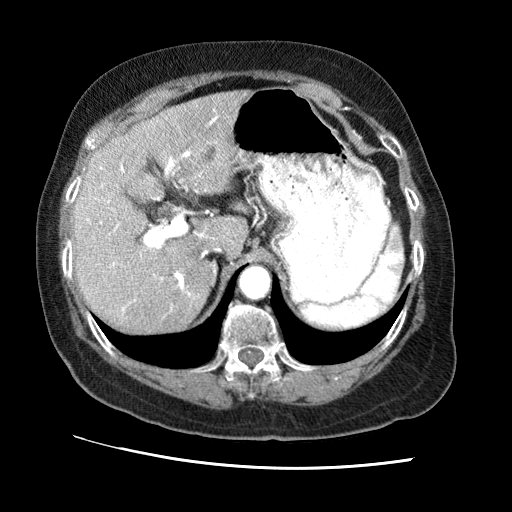
Contrast-enhanced abdominal CT (liver protocol), one axial slice; slice 44 of 65 in the series (ordered by position); reconstruction kernel STANDARD; 120 kVp; soft-tissue window (W 400 / L 40 HU); 2.5 mm slice thickness; 512 × 512 image matrix, field of view 340 × 340 mm. Case-level facts recorded for this patient, not image findings: diagnosis: hepatocellular carcinoma (patient treated with transarterial chemoembolisation; whether this scan precedes or follows treatment is not stated here); TNM stage (as recorded): Stage-II.
Annotated regions visible in this slice (semi-automatically segmented with operator editing):
- liver parenchyma outside the tumour (the mass and vessels are separate outlines, so this box may not span the whole liver): box from (x=72, y=90) to (x=250, y=332) px
- liver vessels: (x=86, y=117)–(x=217, y=312)